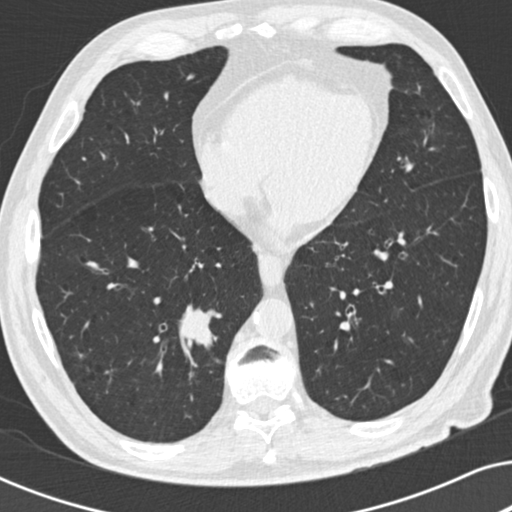
Low-dose screening chest CT, one axial slice; position 83 of 191 along the scan axis; reconstruction kernel B30f; lung window (W 1500 / L -600 HU); 2 mm slice thickness; 512 × 512 image matrix, field of view 330 × 330 mm.
Annotated regions visible in this slice (outlined manually by an expert reader):
- lesion 1 (tumor, lower lobe of right lung): bounding box (x1, y1, x2, y2) in pixels: (182, 307, 217, 353)